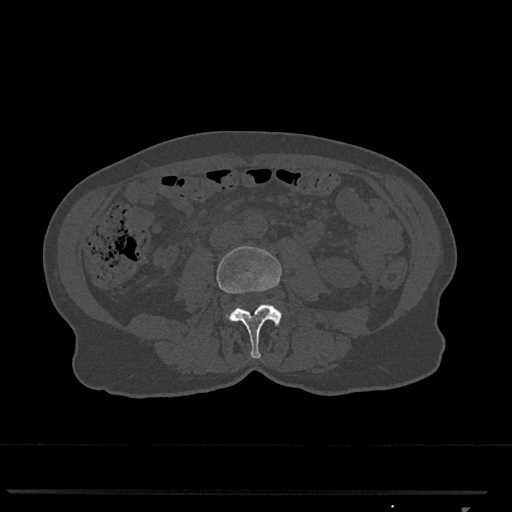
CT including the spine, one axial slice; bone window (W 1800 / L 400 HU); 0.5 mm slice thickness; 512 × 512 image matrix, field of view 380 × 380 mm. Female patient, age 62 years. From the clinical record (not read from this slice): primary cancer: renal.
Annotated regions visible in this slice (semi-automatically segmented with operator editing):
- L3 vertebra: bounding box <217,246,282,359> (left, top, right, bottom; pixels)